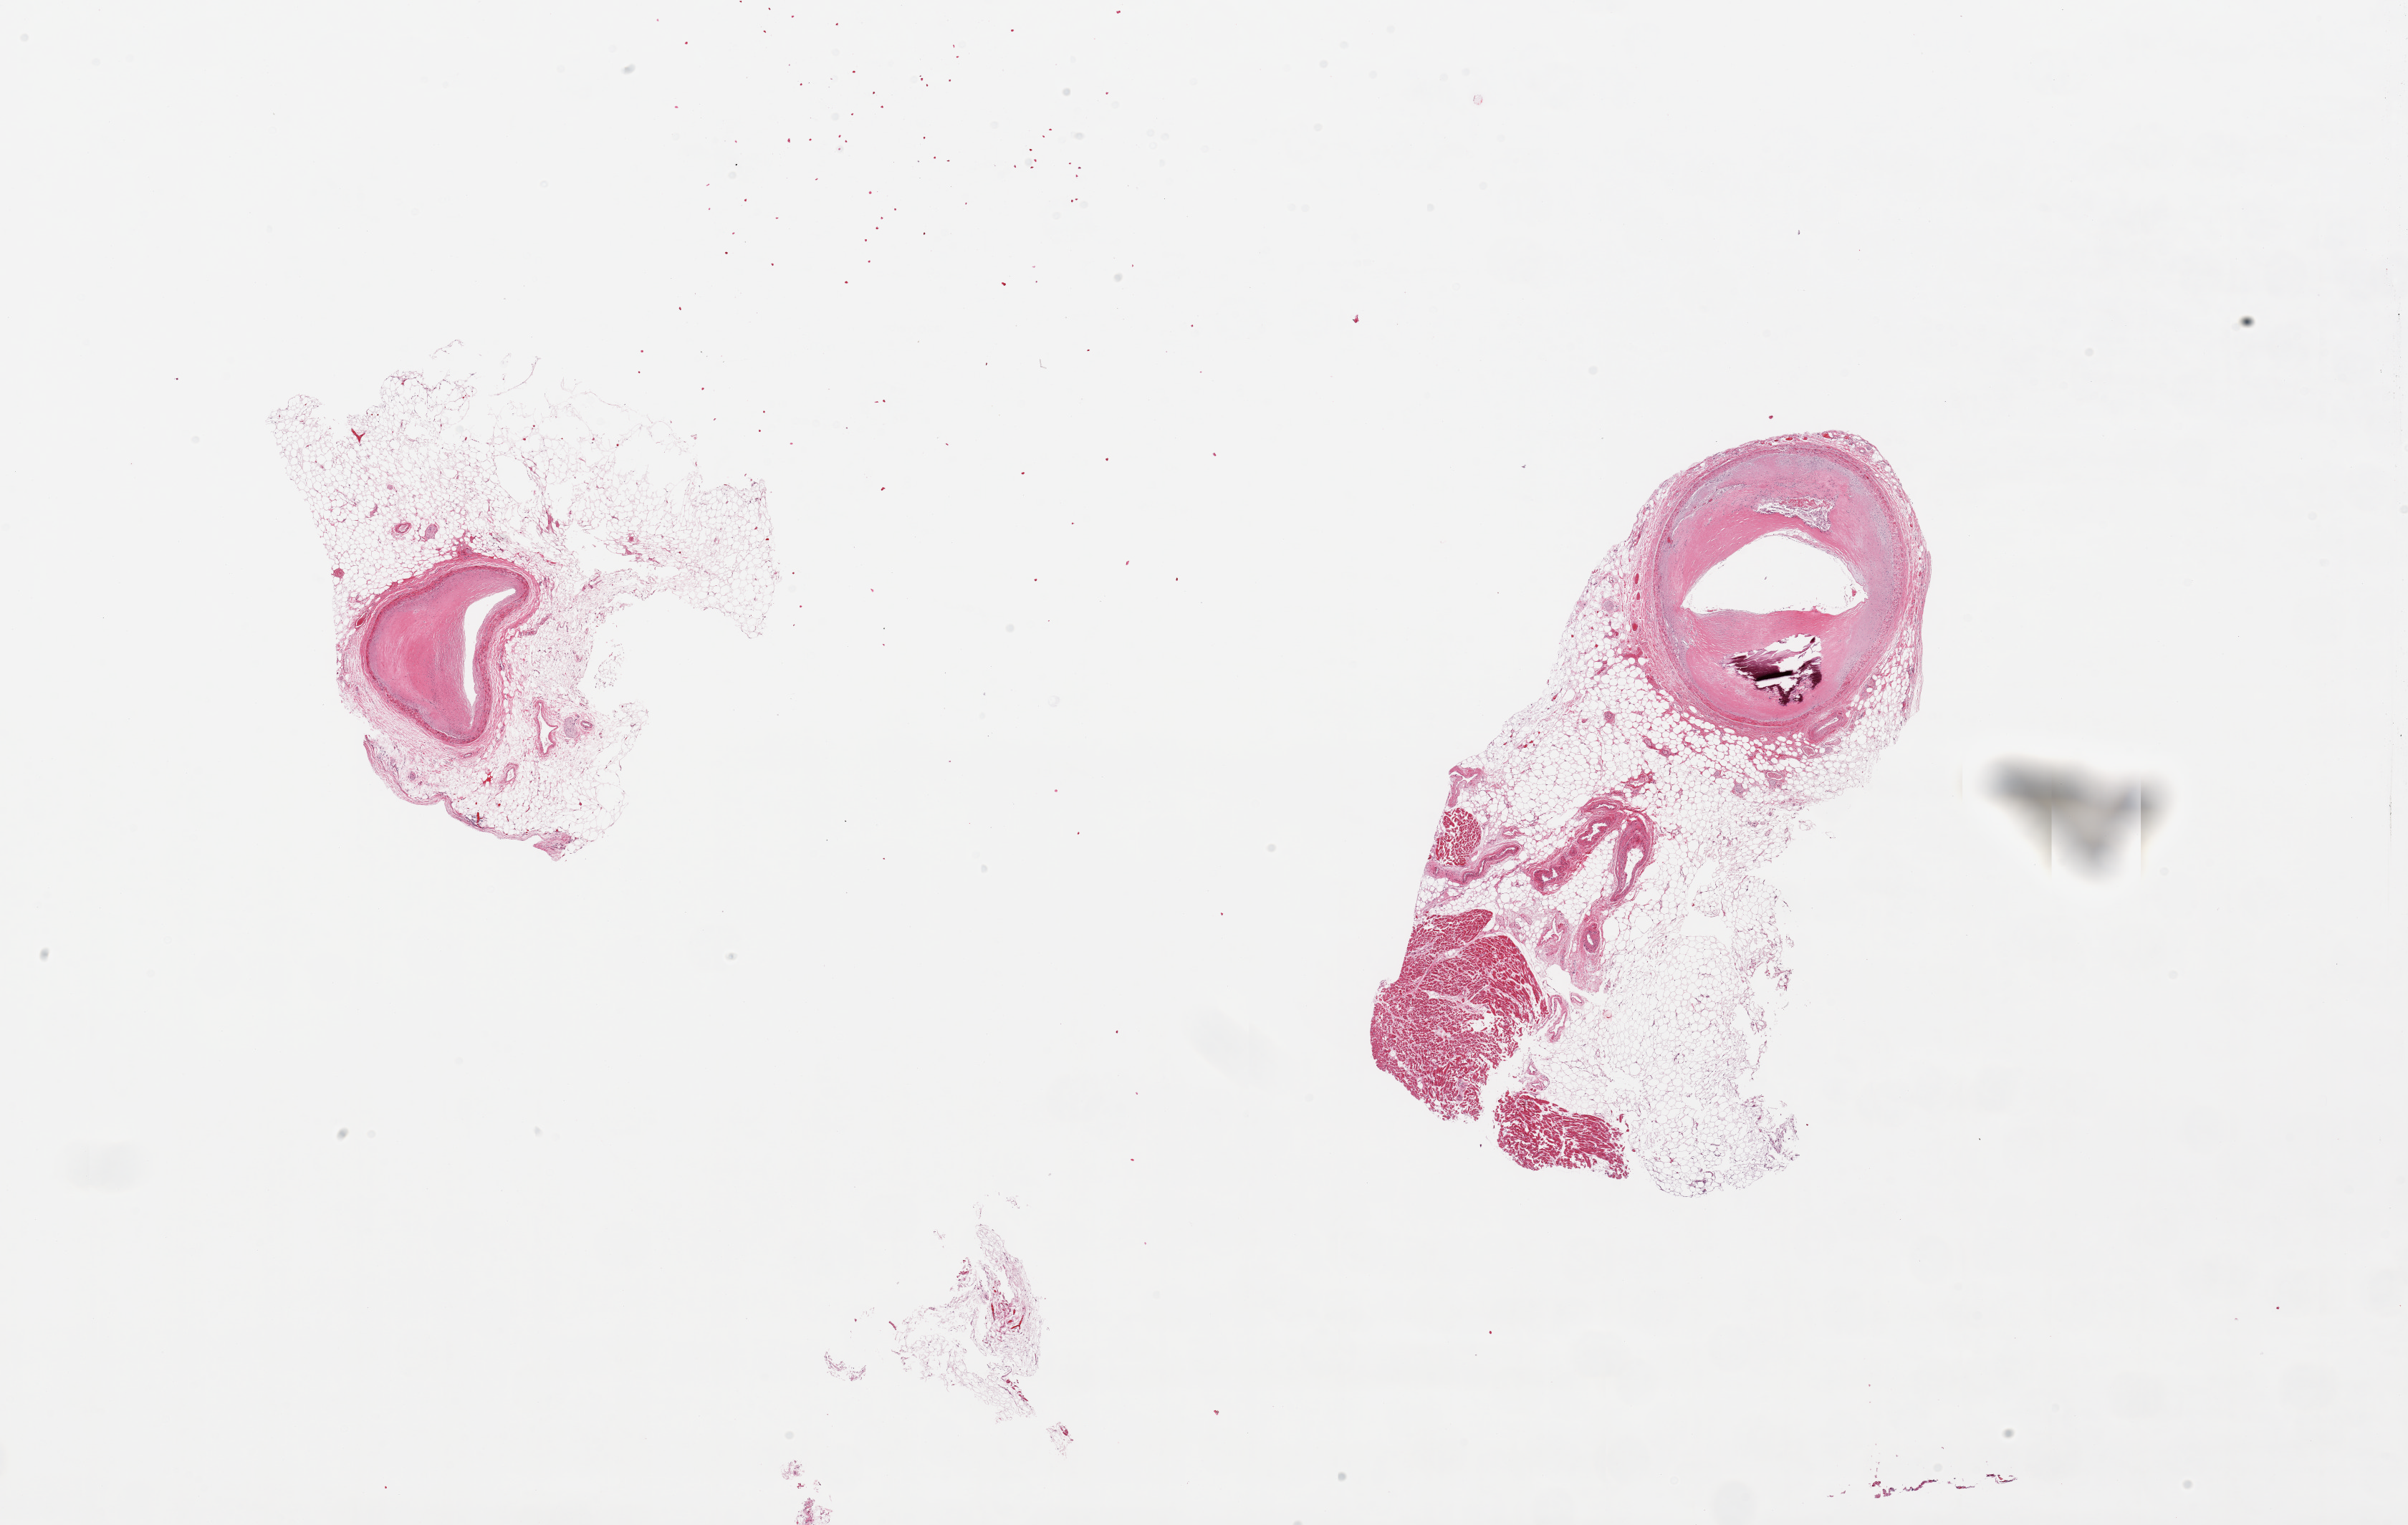
Digitized haematoxylin and eosin-stained section — a low-resolution overview of the entire scanned area, about 26.6 x 16.8 mm (slide scanned at 20x); PAXgene-fixed, paraffin-embedded tissue; target tissue: coronary artery; tissue donor sample.
* review note (as recorded): 2 pieces, subtotally occlusive focally calcified atherosis, large adherent nubbins of fat/myocardium up to ~5mm